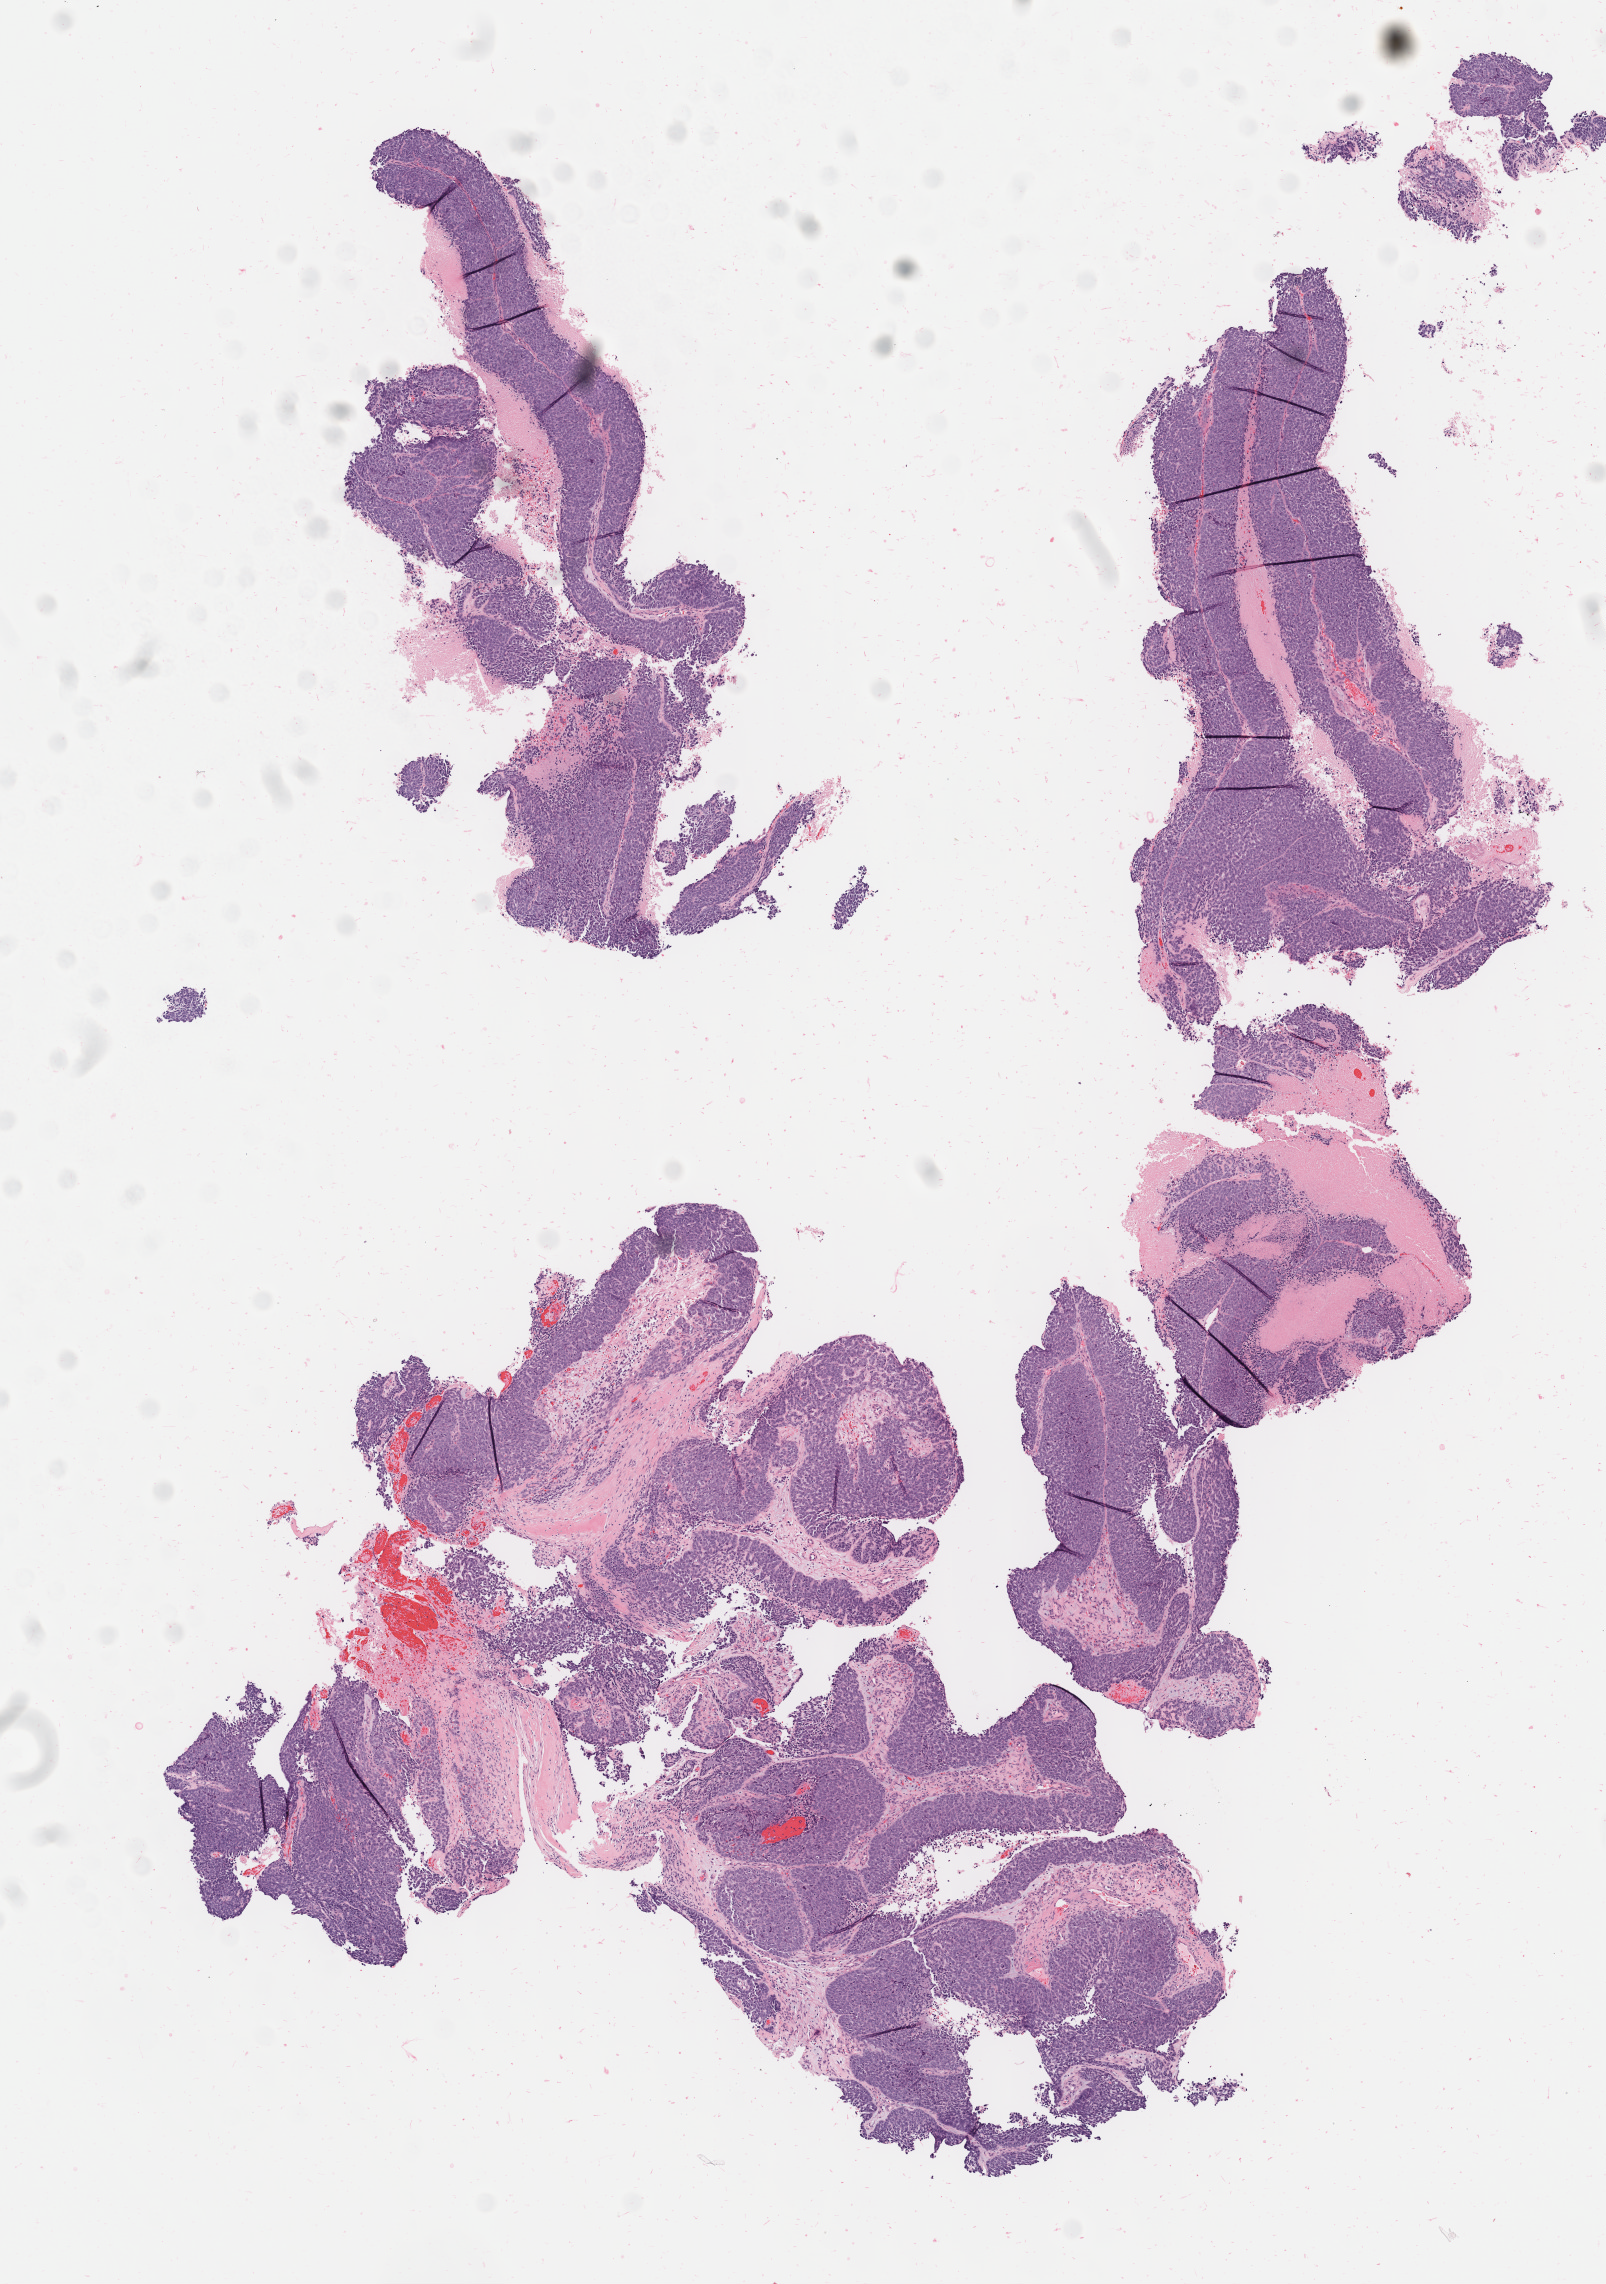
Digitized H&E-stained section, low-resolution overview of the scanned area, about 6.4 x 9.1 mm, specimen: tumor tissue, anatomic site: cervix. Female patient, 64 years old.
Diagnosis: Squamous cell carcinoma, large cell, nonkeratinizing, NOS.